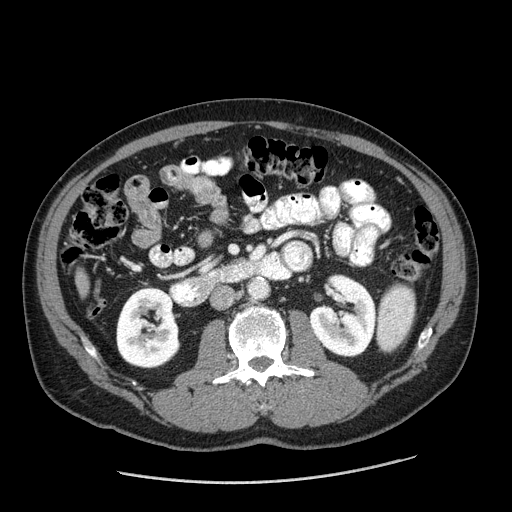
Contrast-enhanced abdominal CT (liver protocol), one axial slice; slice 45 of 198 in the series (ordered by position); 120 kVp; one of 2 acquisitions stored at this slice position; soft-tissue window (W 400 / L 40 HU); 2.5 mm slice thickness; 512 × 512 image matrix, field of view 400 × 400 mm. From the clinical record (not read from this slice): diagnosis: hepatocellular carcinoma (patient treated with transarterial chemoembolisation; whether this scan precedes or follows treatment is not stated here); TNM stage (as recorded): Stage-II; Child-Pugh class: A; tumour differentiation: moderately differentiated; tumour nodularity: multinodular.
Outlined on this slice (semi-automatic segmentation, software-assisted and operator-edited):
- liver parenchyma outside the tumour (the mass and vessels are separate outlines, so this box may not span the whole liver): bounding box <76,270,88,296> (left, top, right, bottom; pixels)